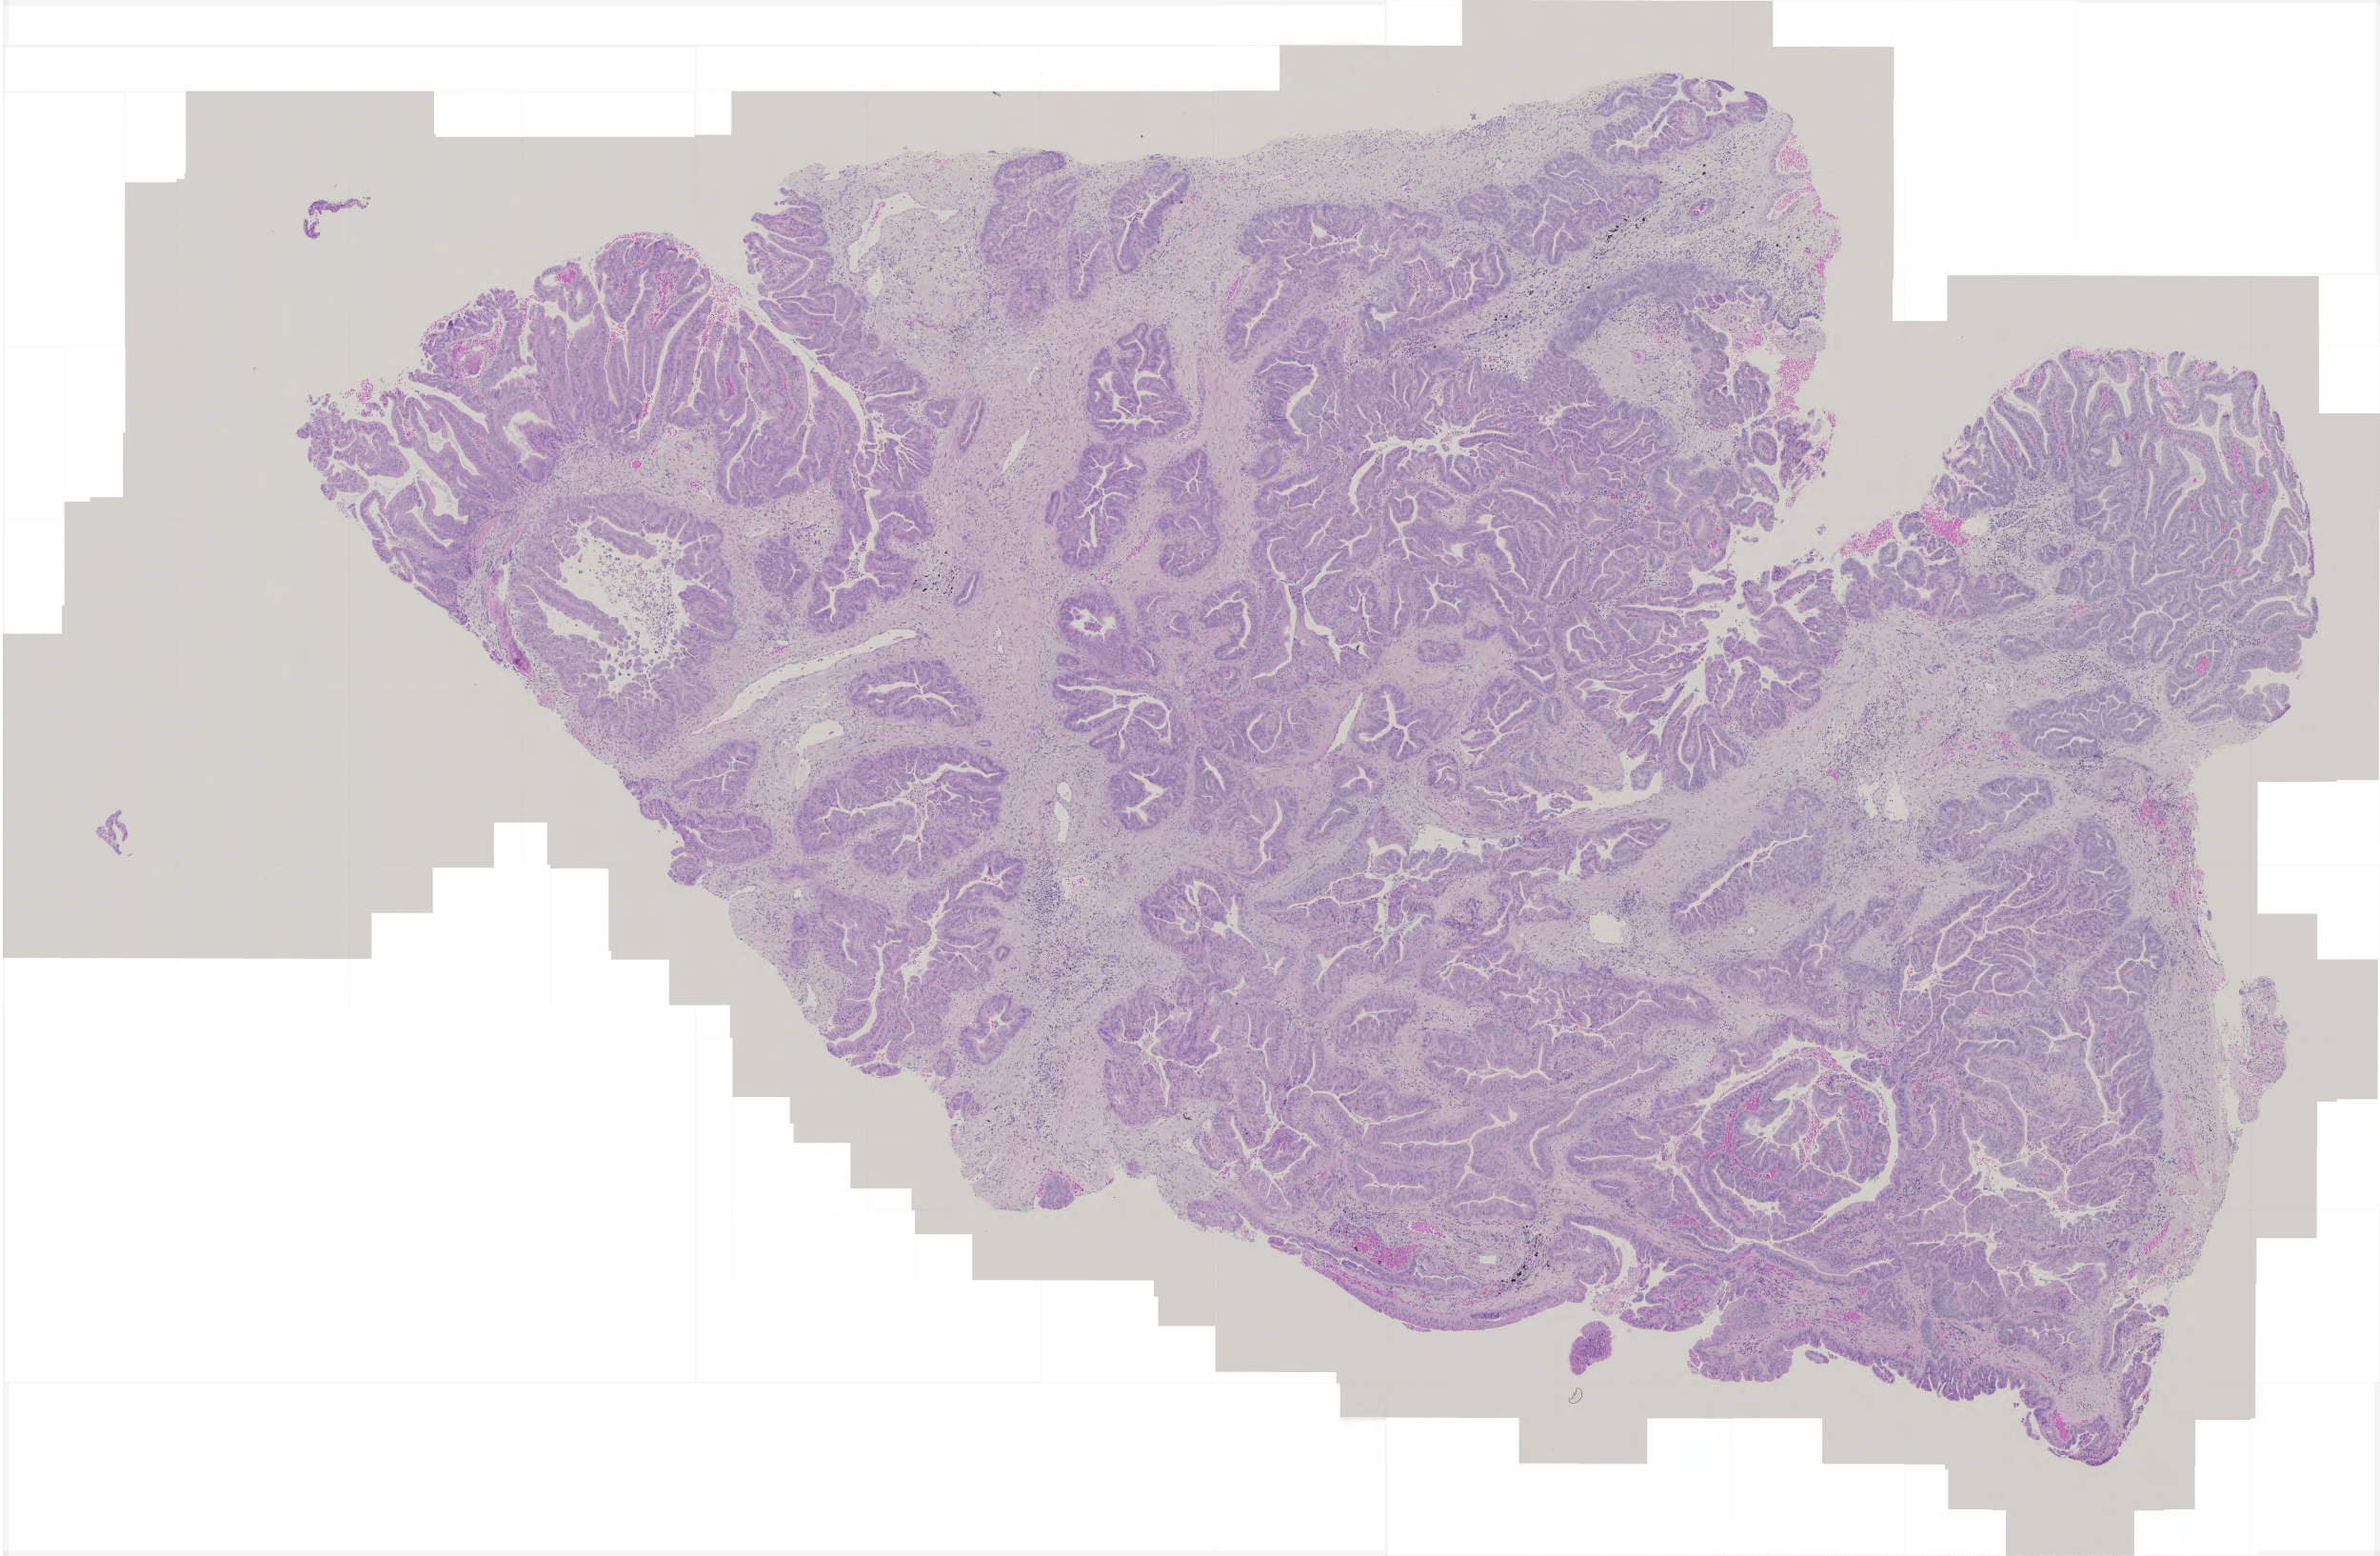
H&E-stained whole-slide image — low-resolution overview of the scanned area, about 5.0 x 3.3 mm; formalin-fixed paraffin-embedded (FFPE) diagnostic section; lung, primary tumour sample. Patient: male, age at initial diagnosis 60 years.
Laterality: left. Diagnosis: Adenocarcinoma, NOS. AJCC pathologic stage: IIIA. TNM: T3 N2 M0.